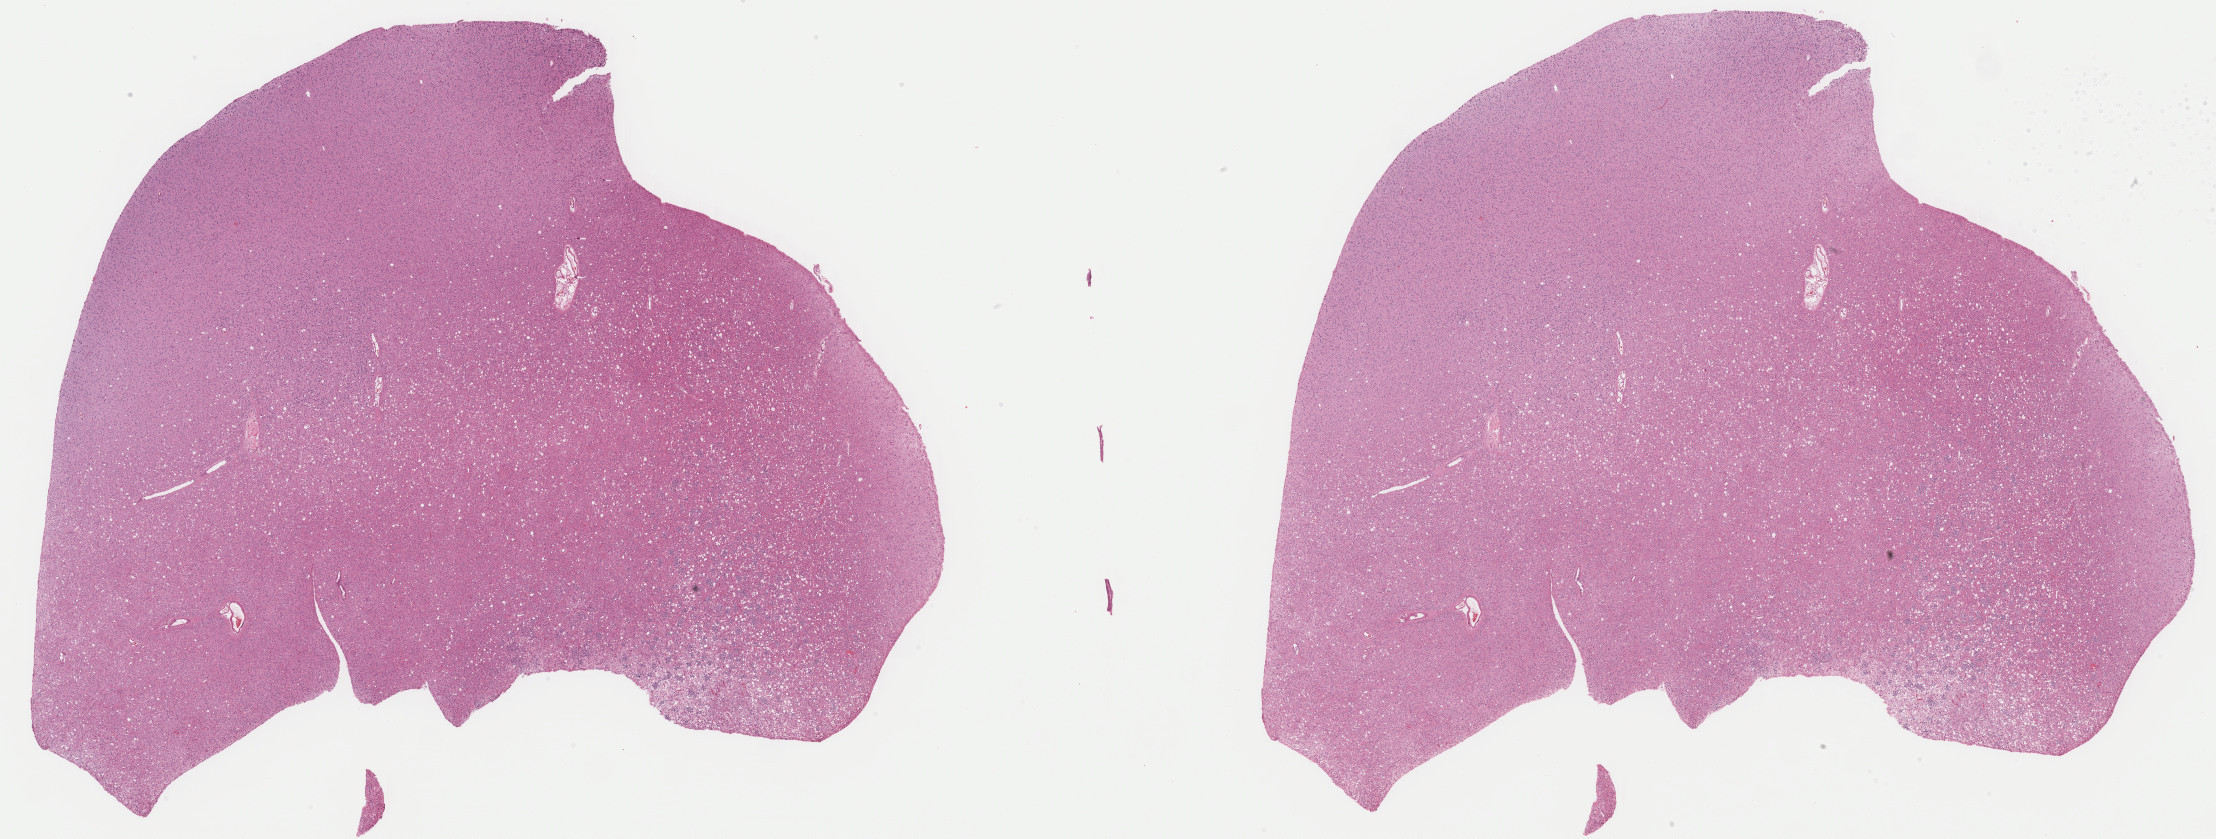
Hematoxylin and eosin (H&E) stained whole-slide image — shown as a low-resolution overview of the whole scanned area (about 34.9 x 13.2 mm, acquisition: 40x scan), formalin-fixed paraffin-embedded (FFPE) diagnostic section, primary tumour sample from the brain. Female, age 53 years at initial diagnosis. Histologic grade: G2 (moderately differentiated).
Diagnosis: Mixed glioma (frontal lobe). Laterality: left.